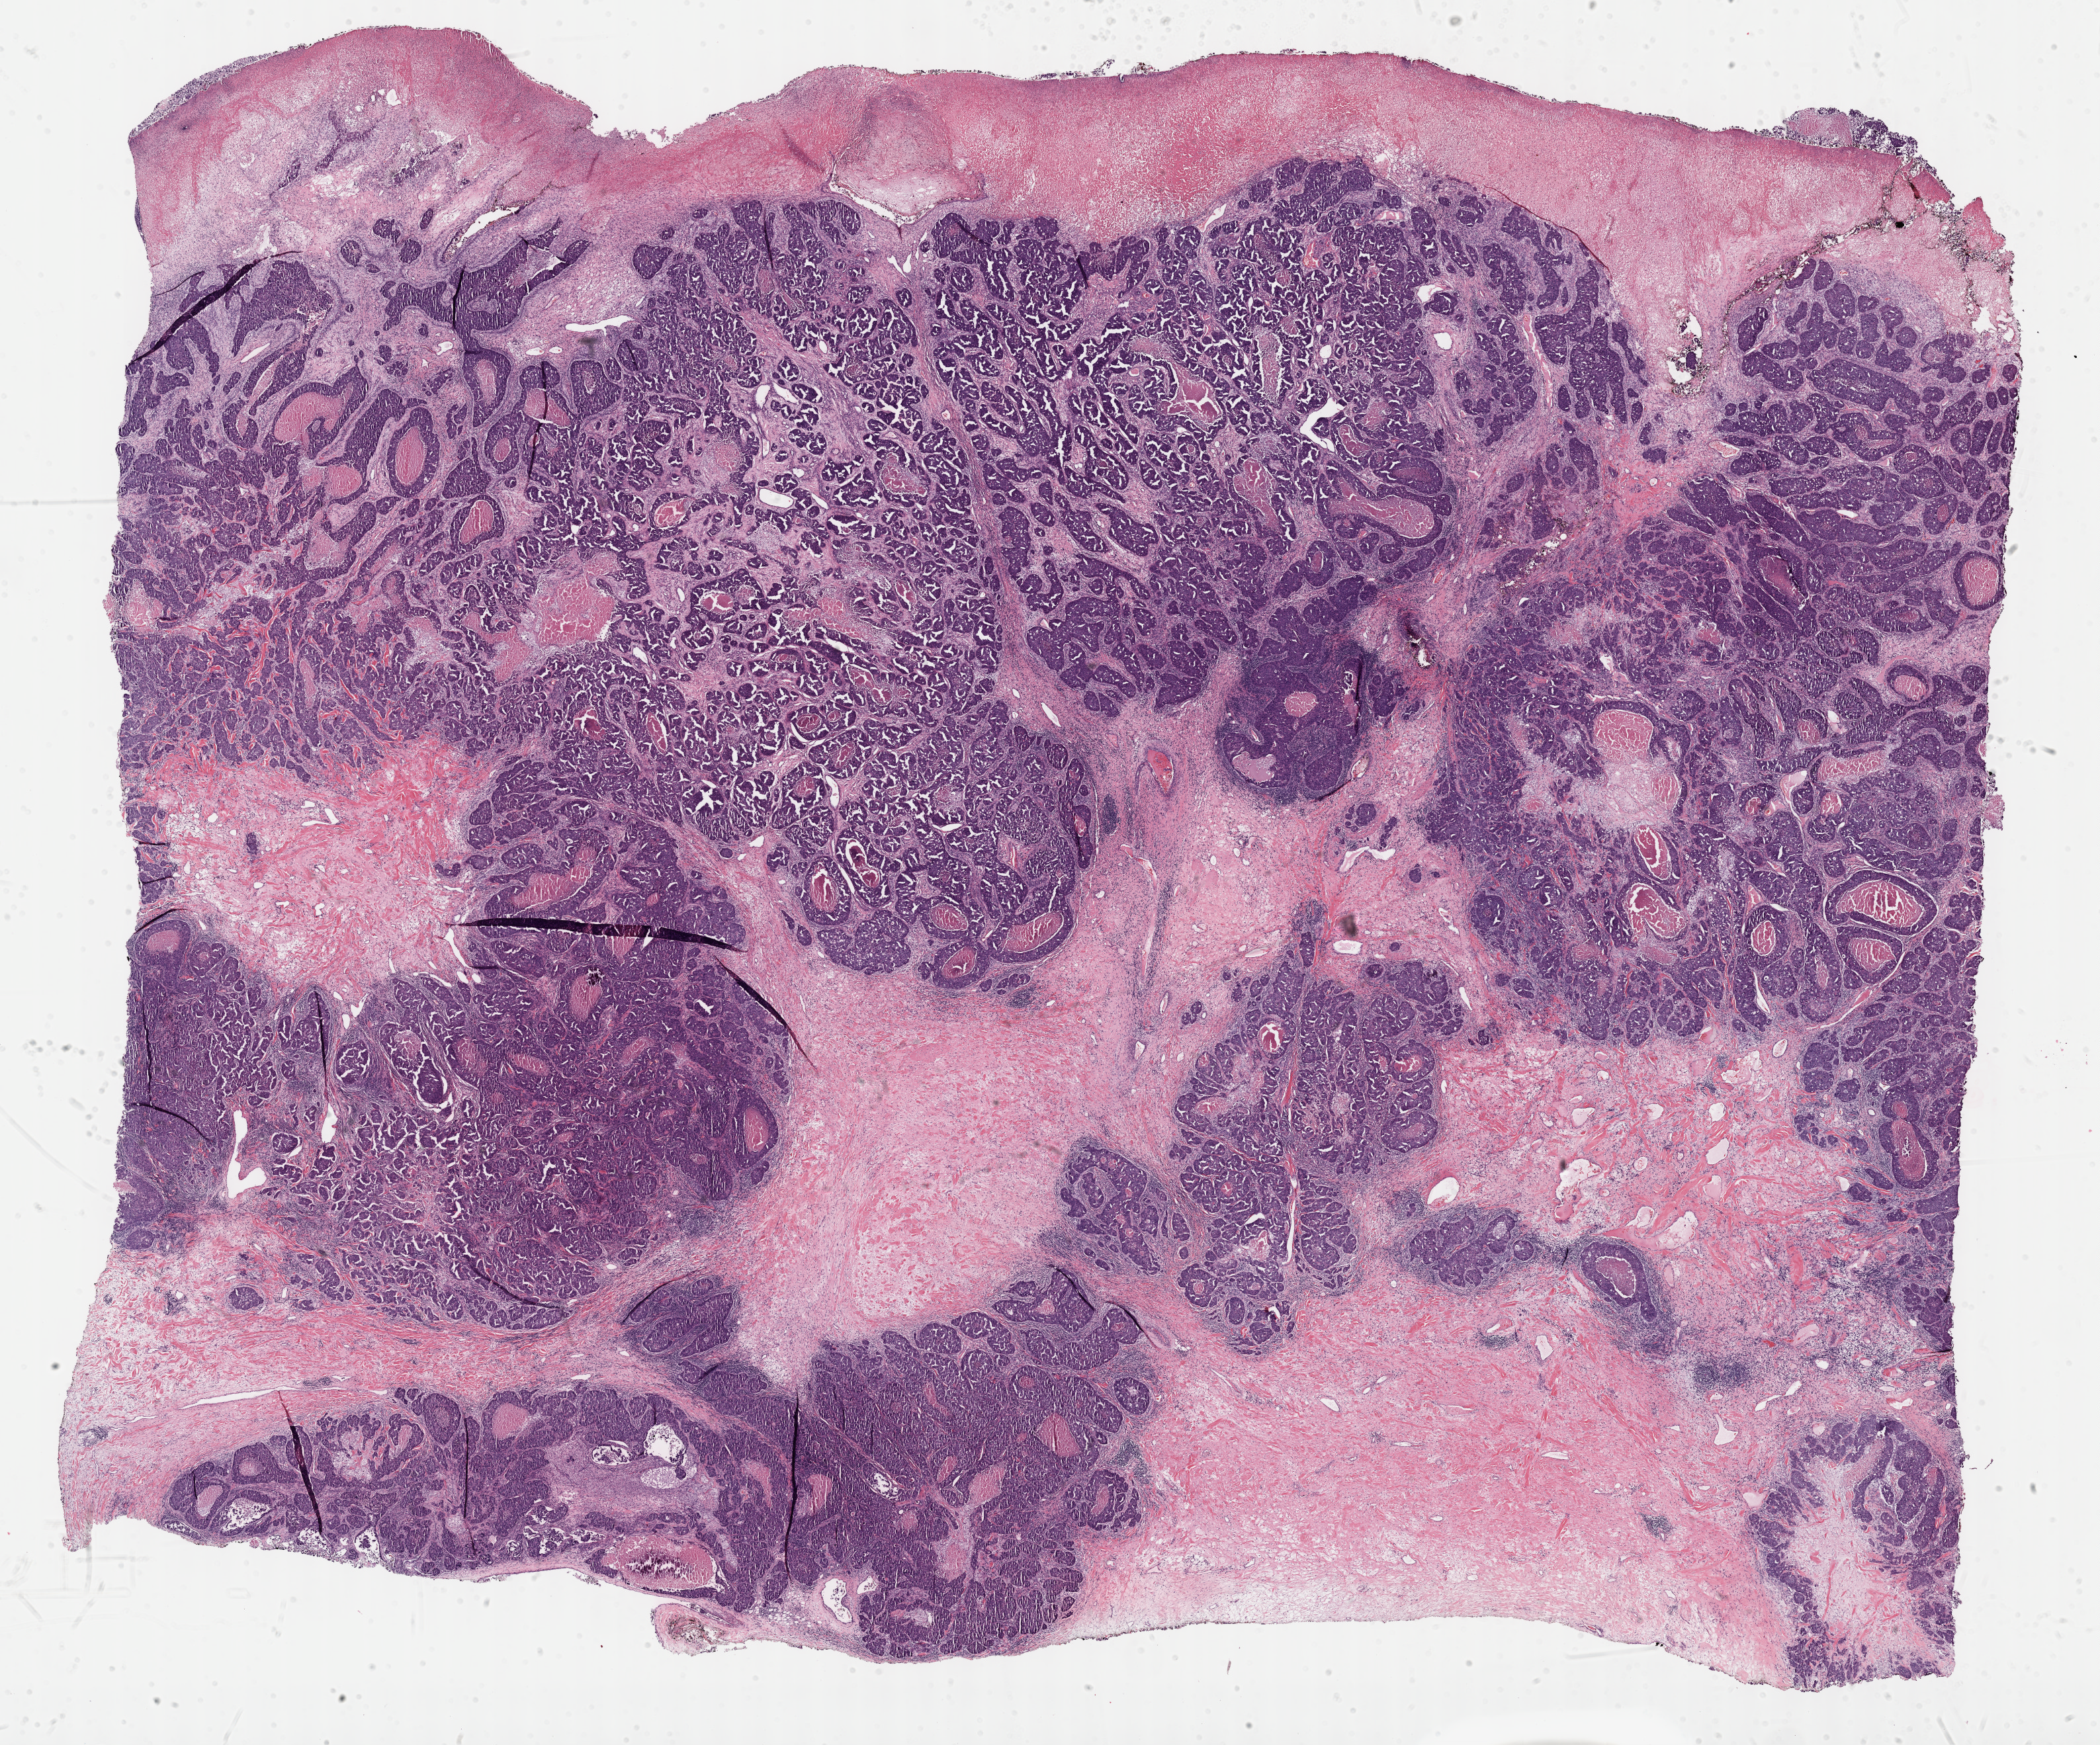
Whole-slide histology image, H&E — low-resolution overview of the scanned area, about 25.7 x 21.3 mm, formalin-fixed paraffin-embedded (FFPE) diagnostic section, sample: primary tumour, breast. Female, age 63 years at initial diagnosis.
- AJCC pathologic stage: IV (7th edition)
- diagnosis: Infiltrating duct carcinoma, NOS